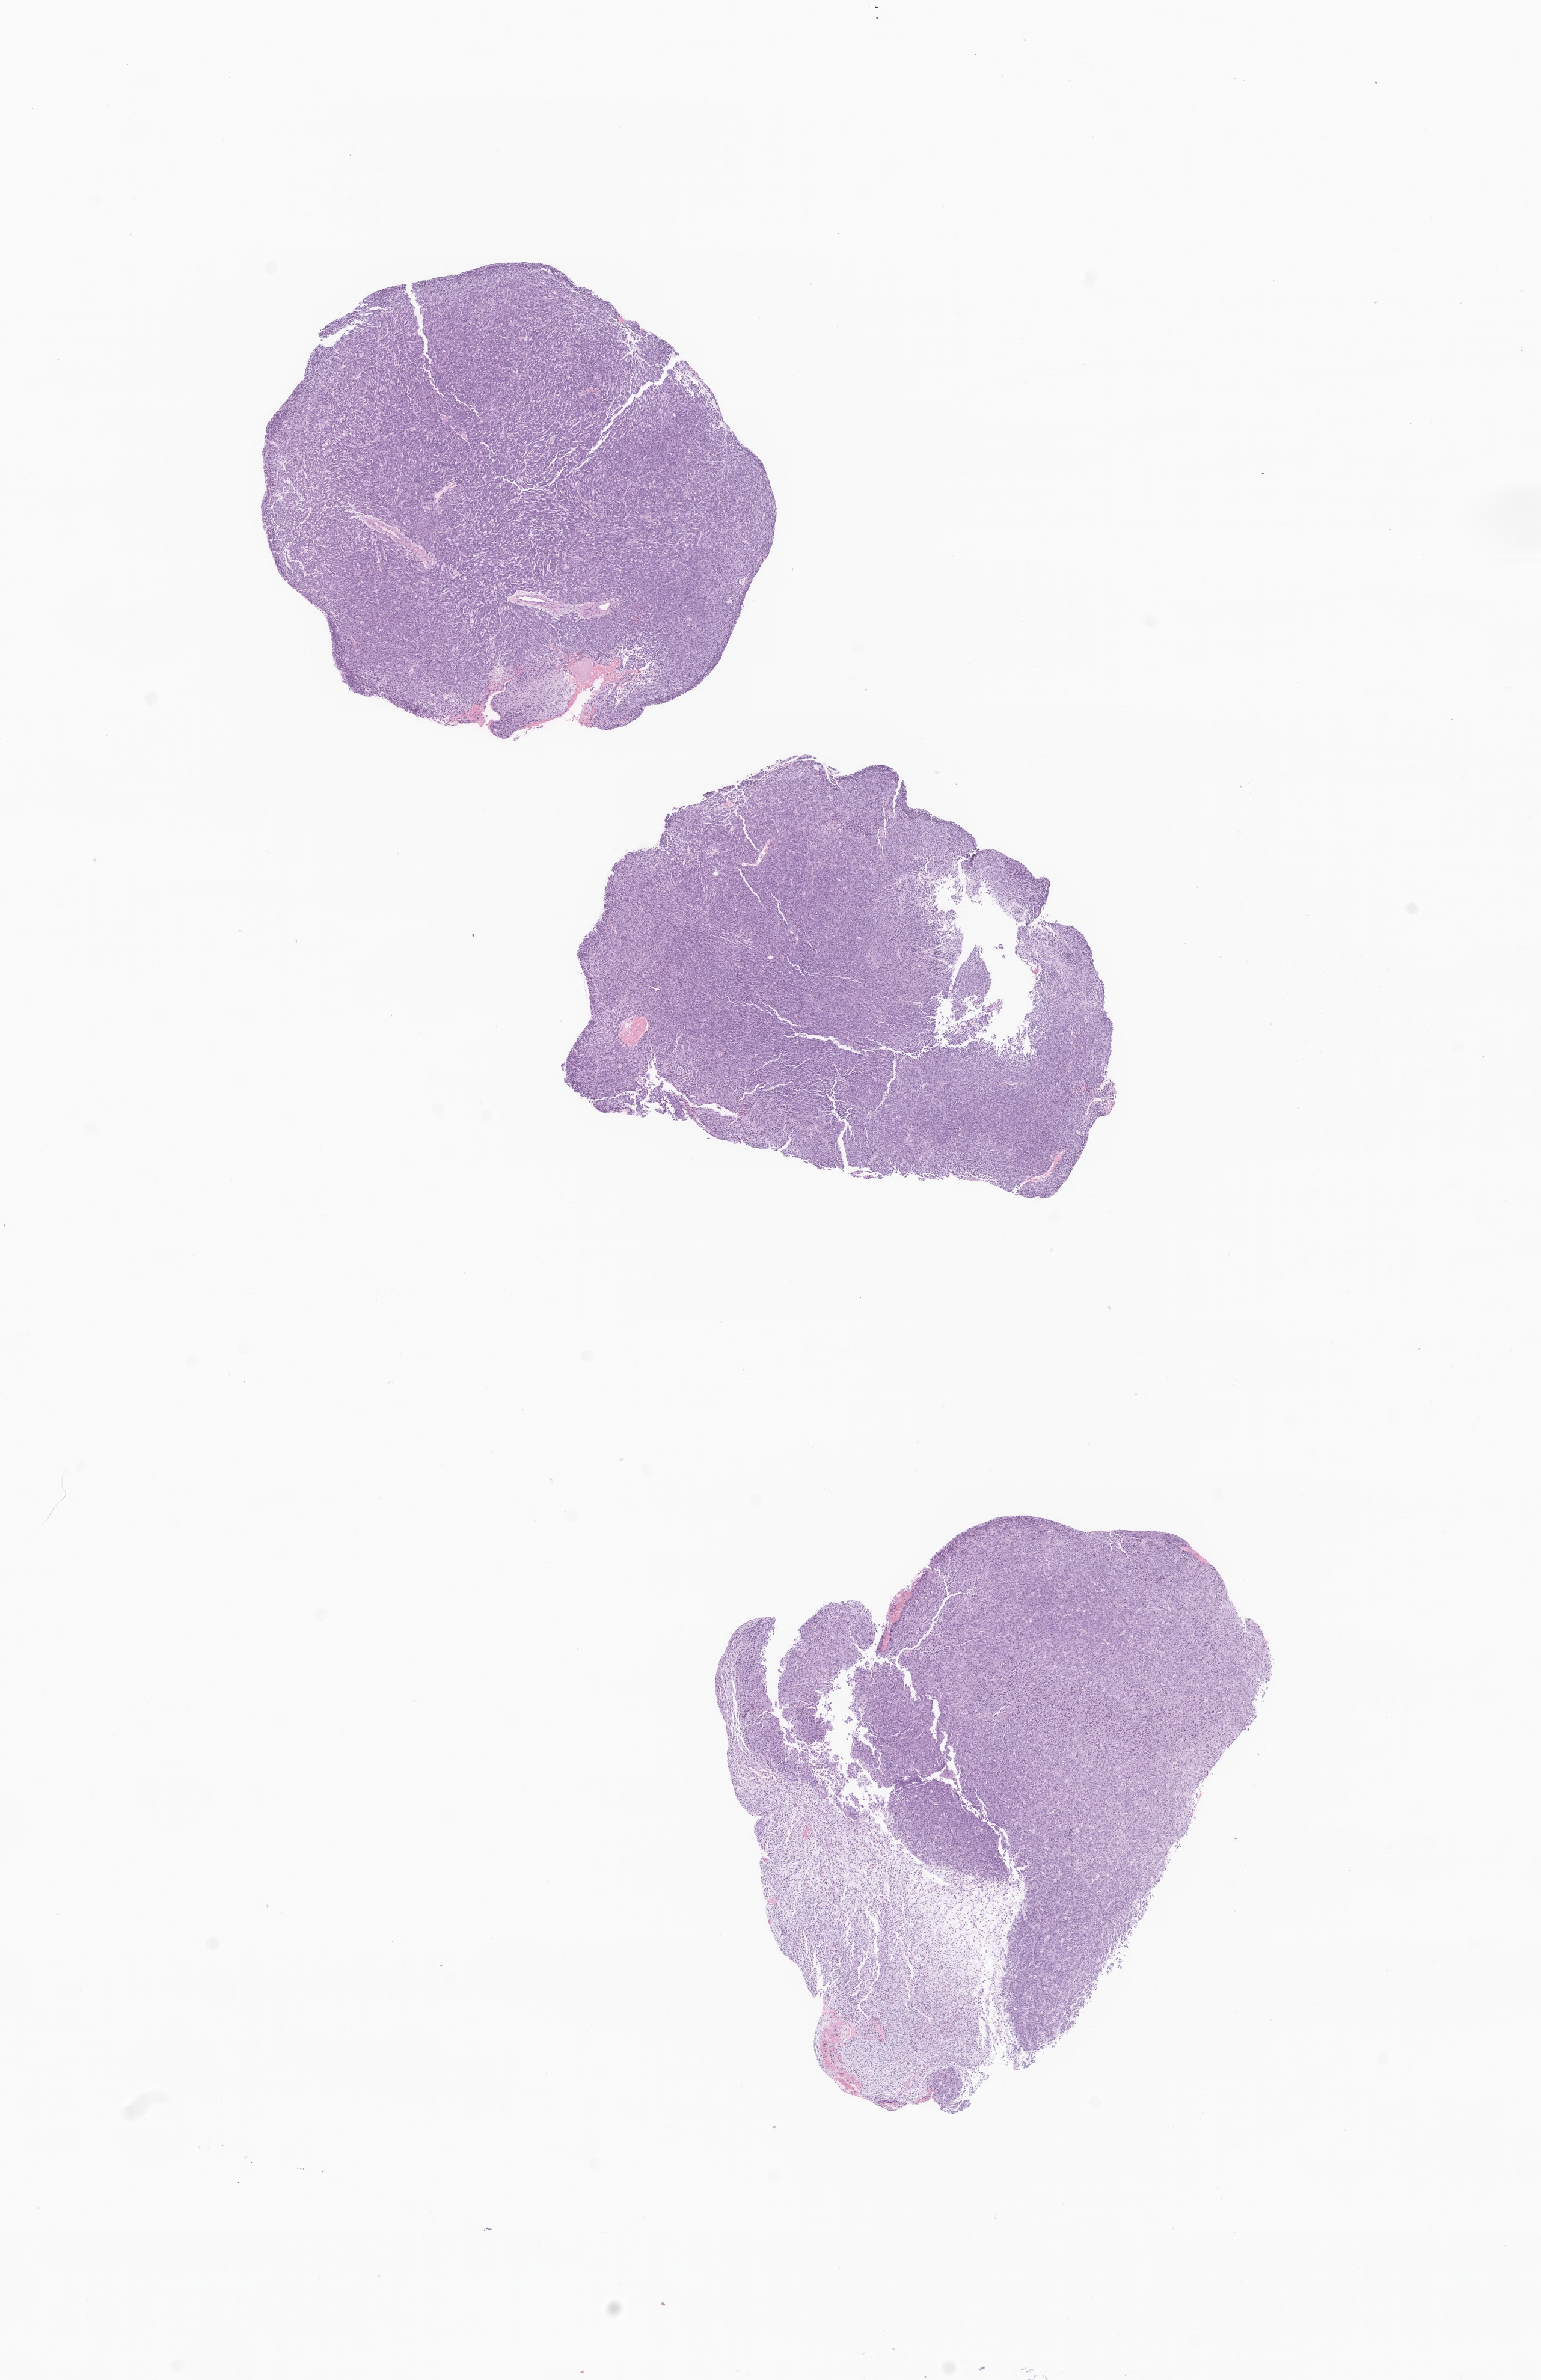
Hematoxylin and eosin (H&E) whole-slide image of tumor tissue from the brain stem, low-resolution overview of the scanned area, about 10.8 x 16.7 mm, formalin-fixed, paraffin-embedded (FFPE) tissue. Male patient, age 66 months (5 years 6 months).
- recorded diagnosis: Rhabdoid tumor, NOS